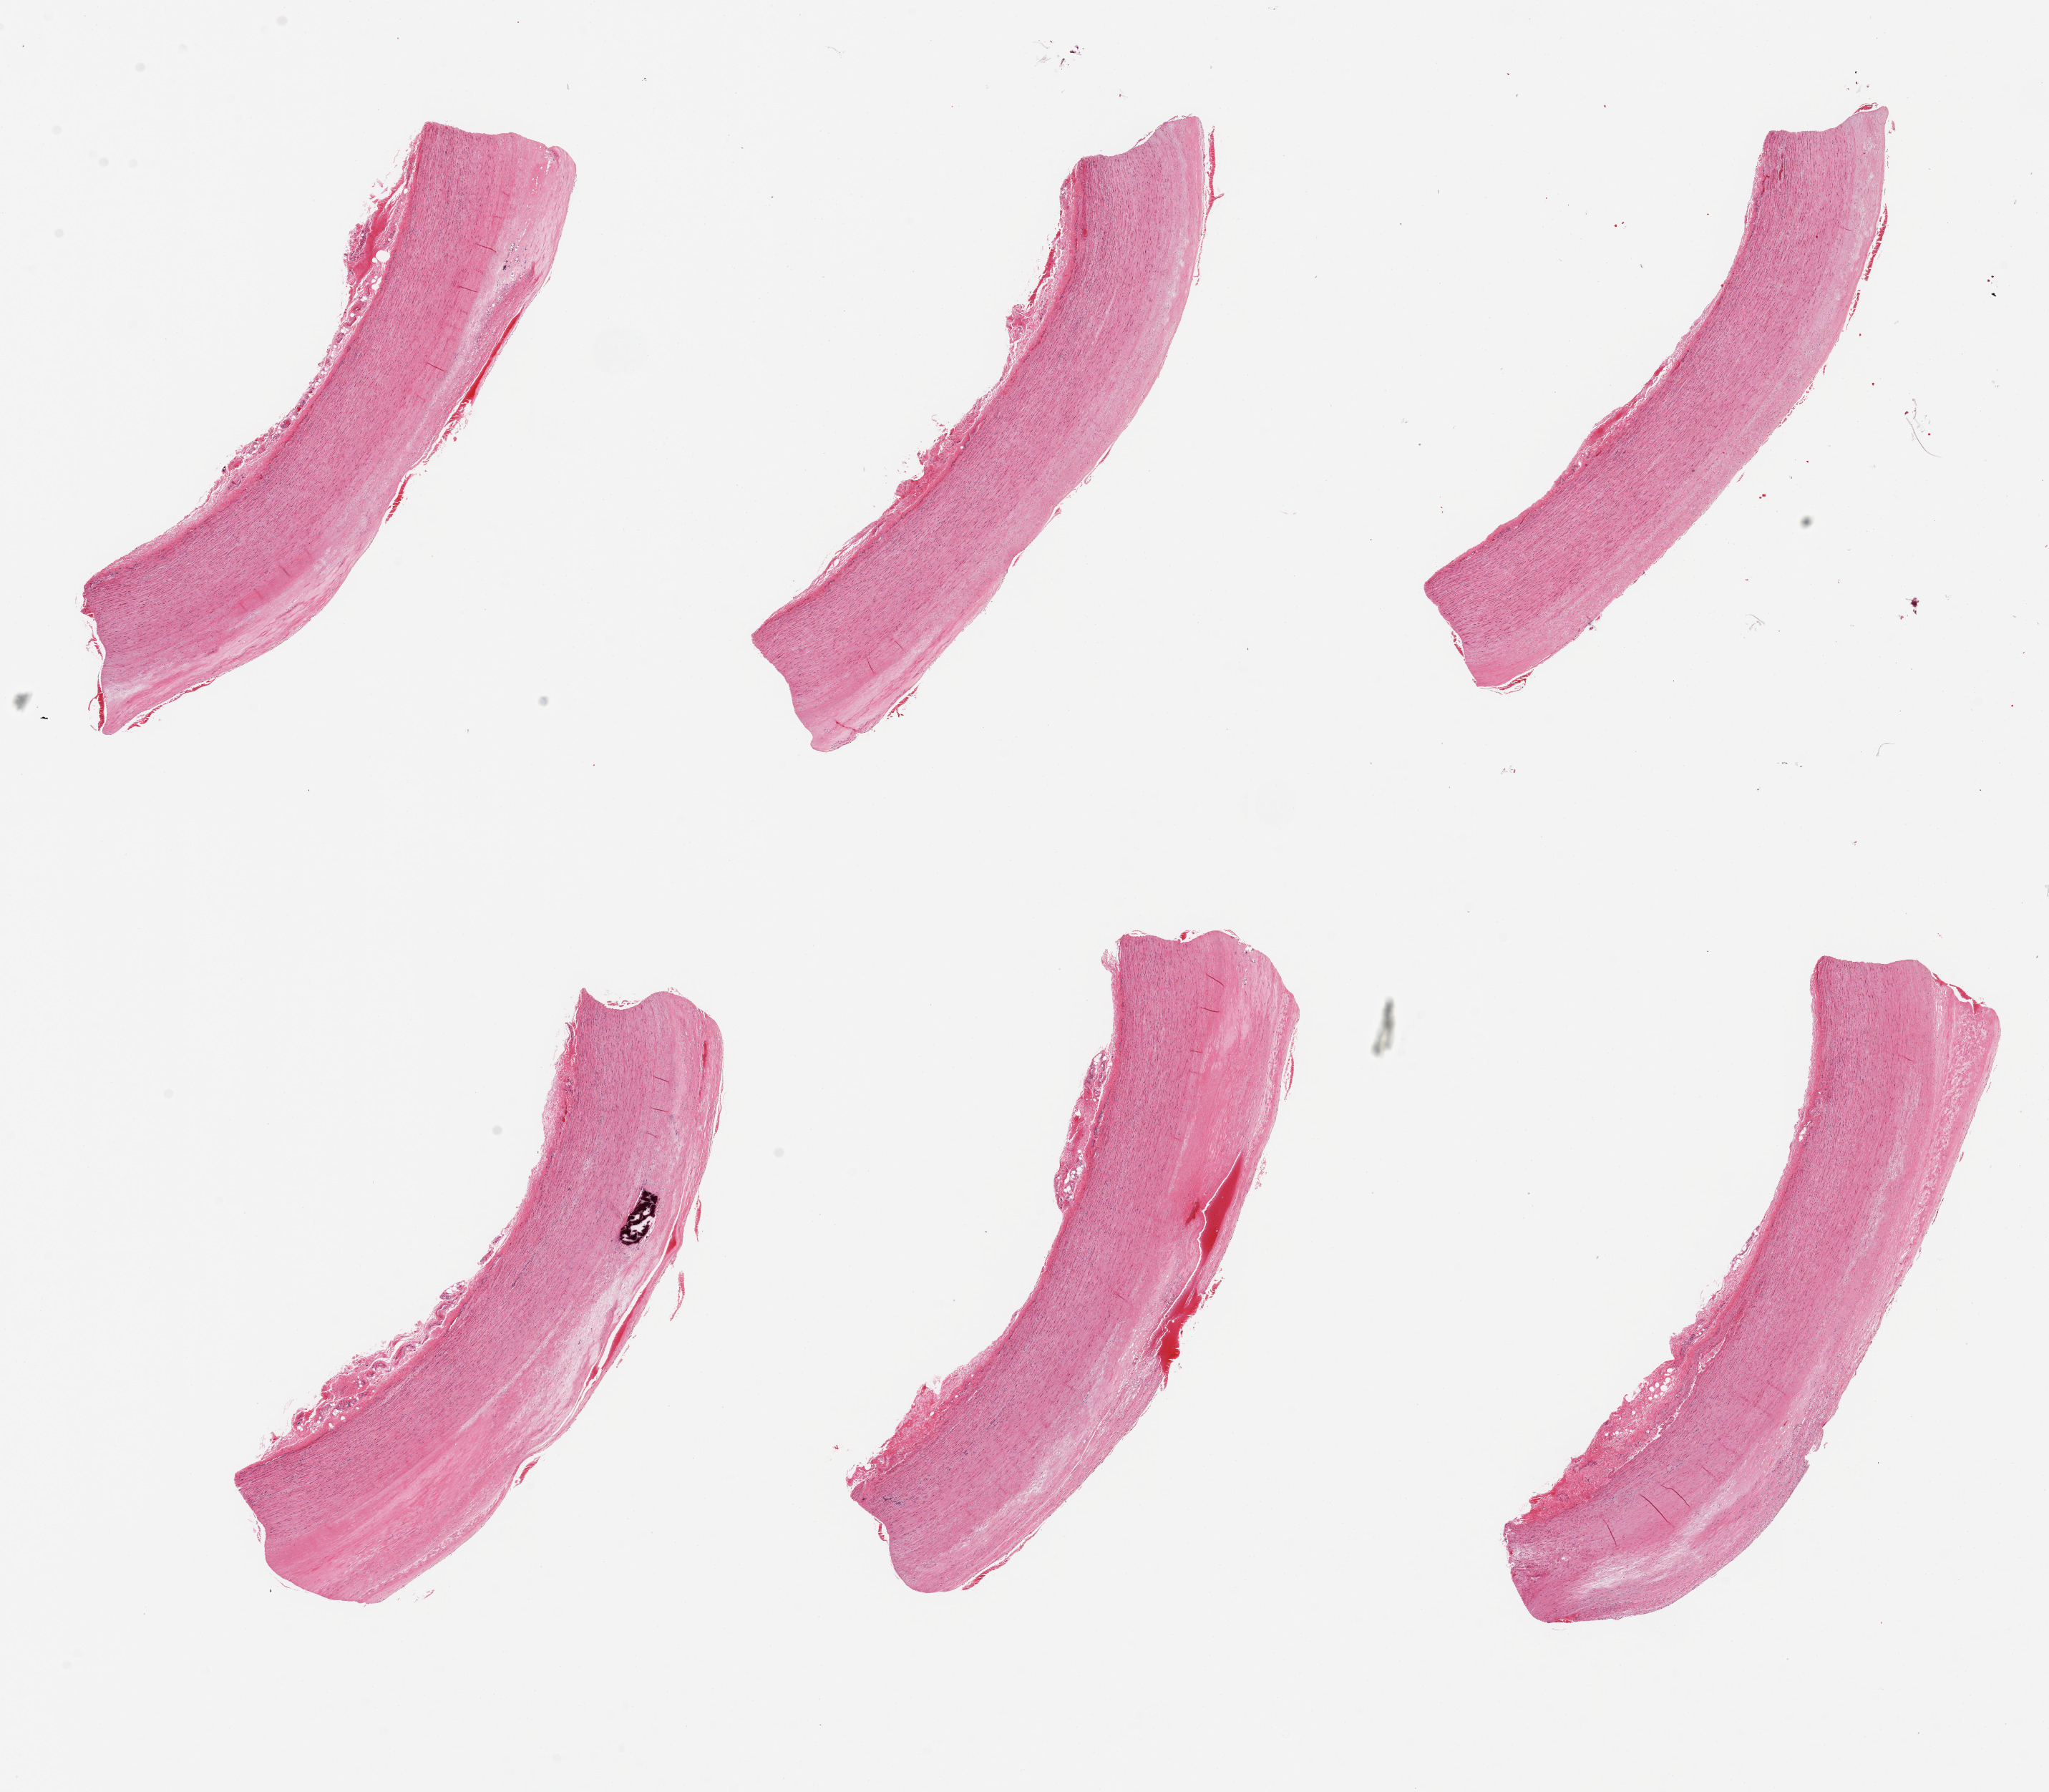
H&E whole-slide image, shown as a low-resolution overview of the whole scanned area (about 22.6 x 19.8 mm). PAXgene-fixed paraffin-embedded (PFPE) section. Section of aorta (target tissue). Tissue donor sample. Male donor.
• review note (as recorded): 6 pieces; intimal hemorrhage in 1 and calcification in 1